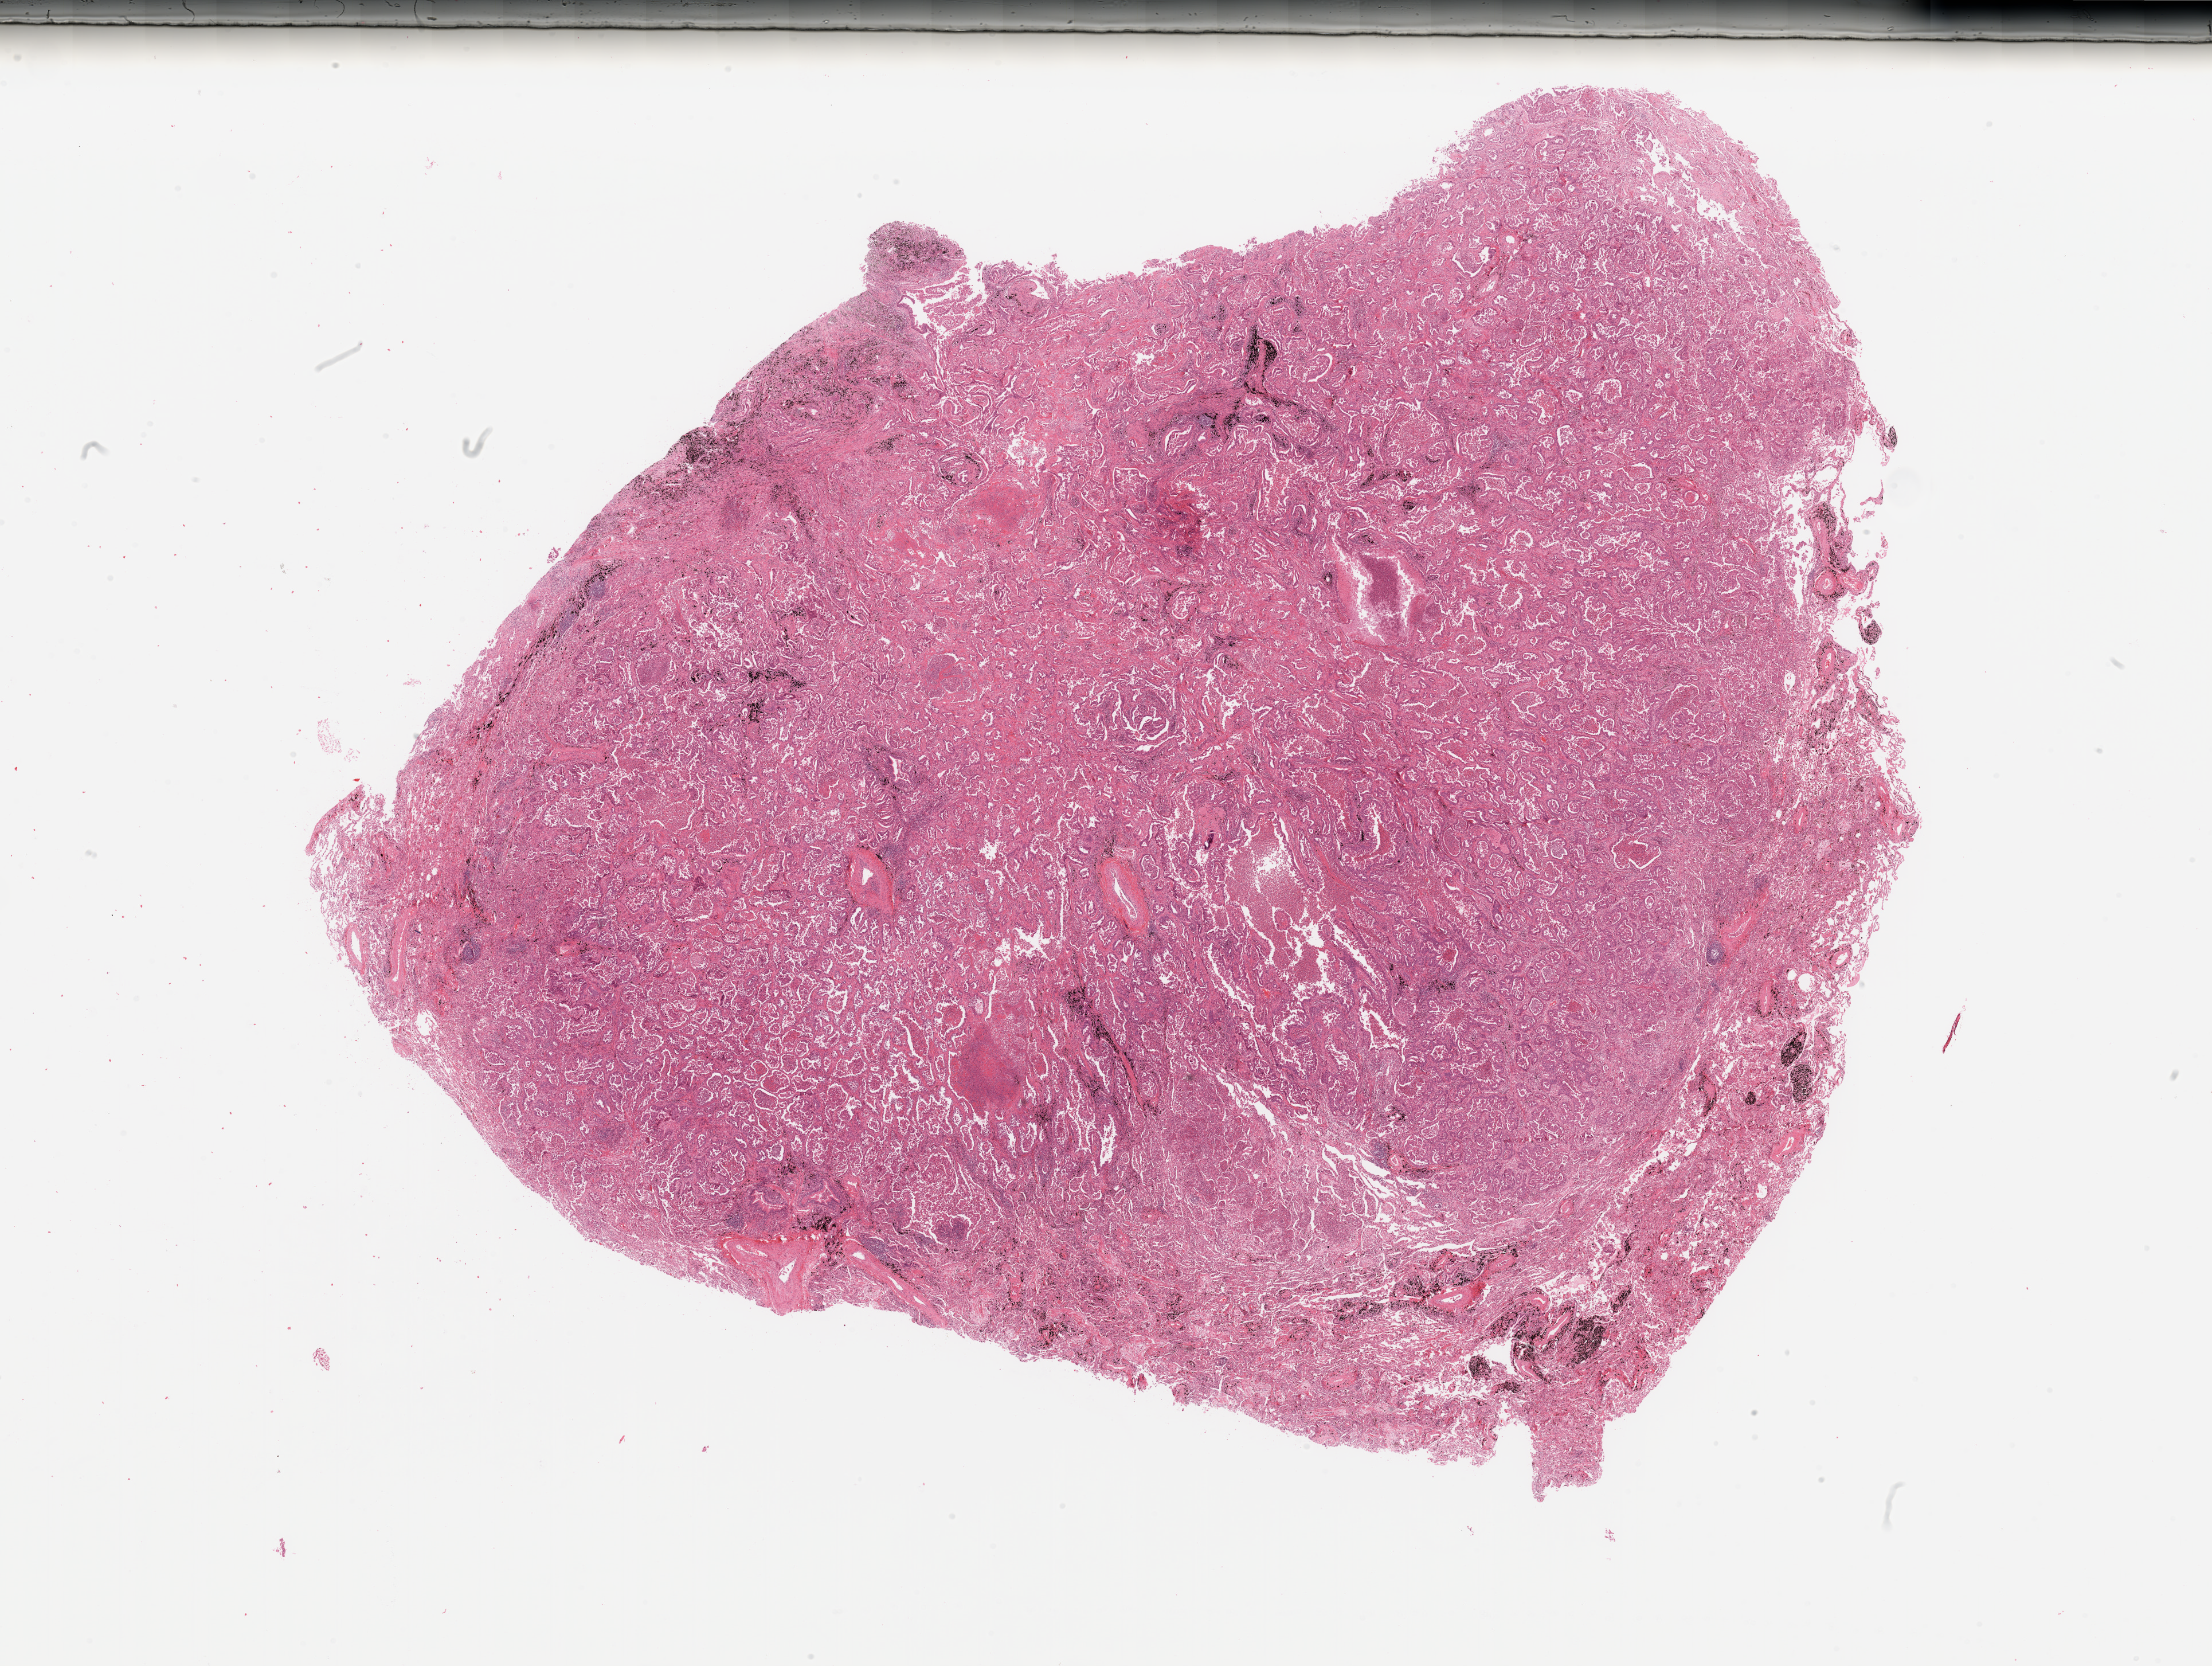
Digitized H&E-stained tissue section (whole slide) — a low-resolution overview of the entire scanned area, about 30.5 x 23.0 mm; tumour tissue sample, lung. 69-year-old male patient. Histologic grade: G2 (moderately differentiated).
- primary tumour site (as recorded): left lower lobe
- diagnosis: Adenocarcinoma, NOS
- AJCC pathologic stage: IB